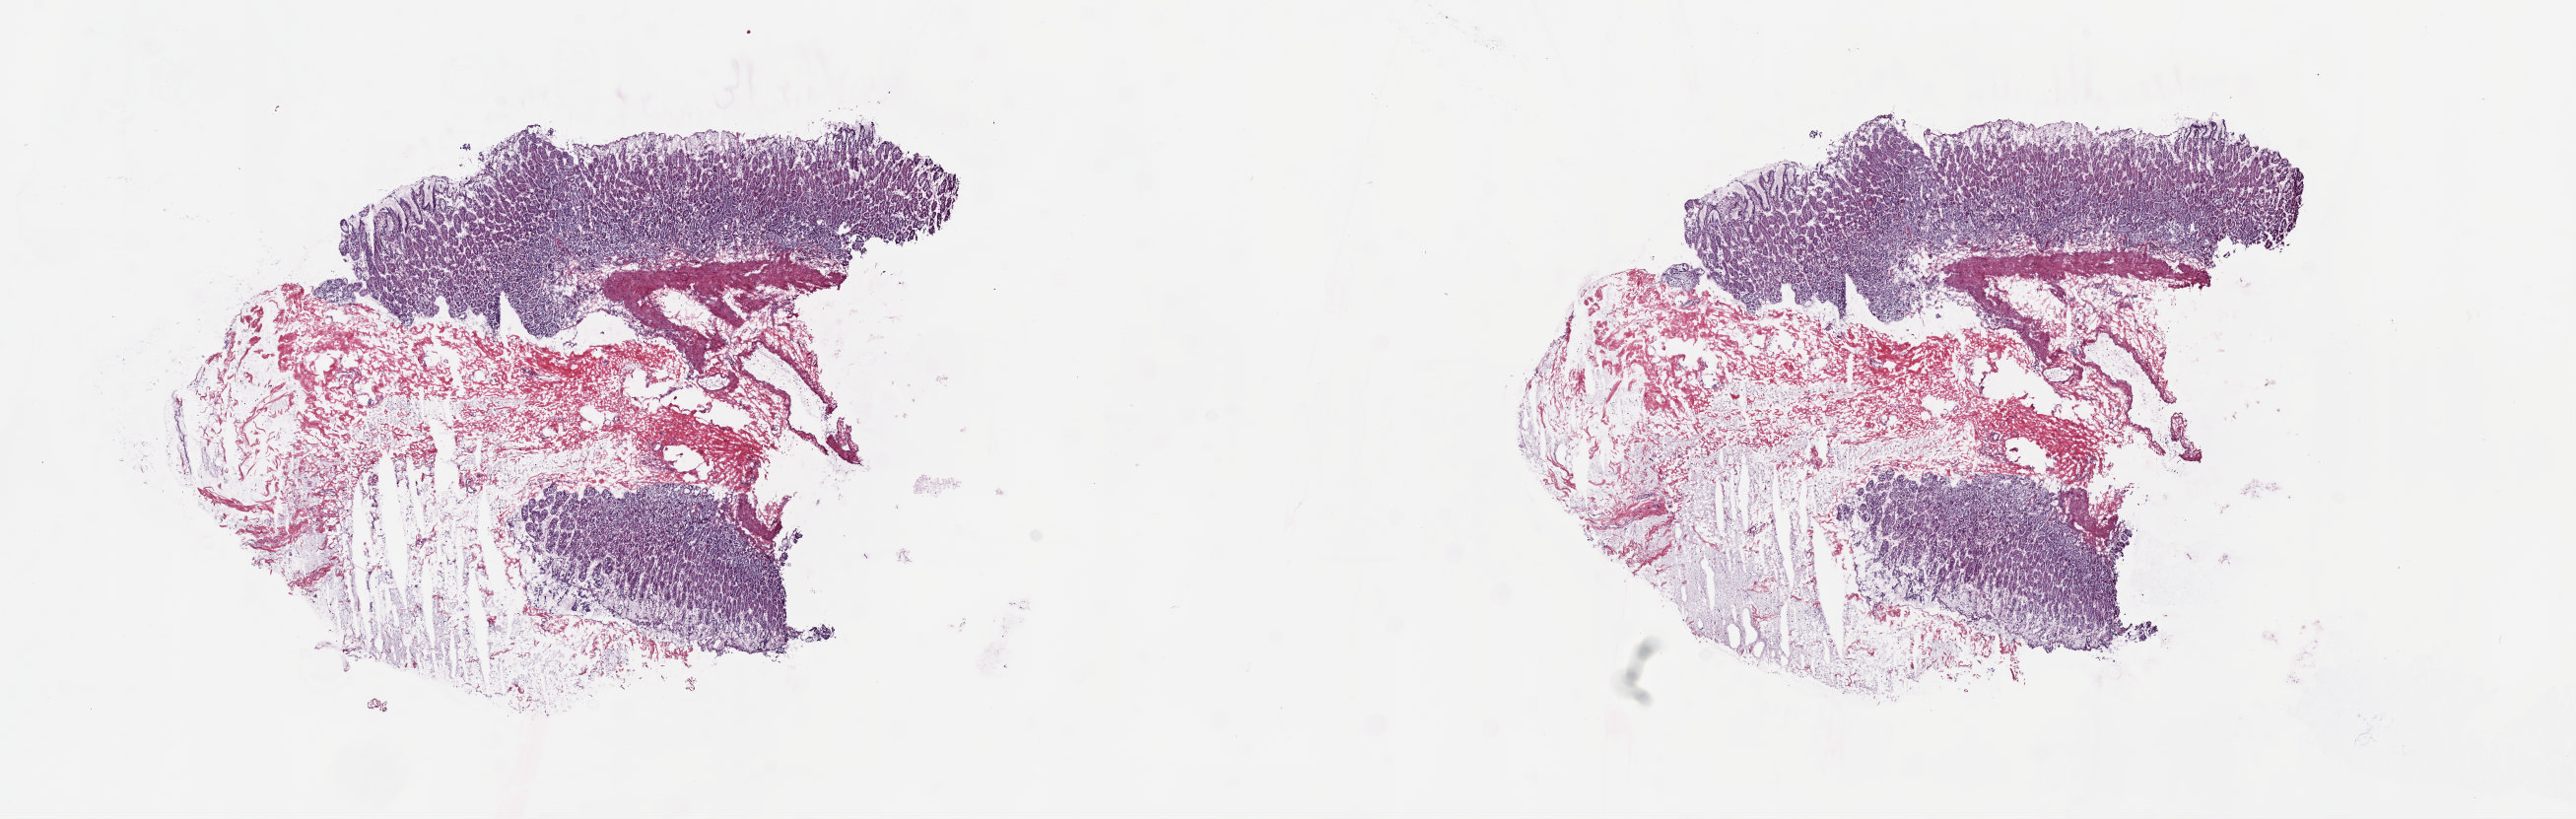
Whole-slide histology image, H&E-stained — whole scanned area (about 20.6 x 6.6 mm) shown as a low-resolution overview, frozen section, sample: solid tissue normal (non-tumour tissue), esophagus. Patient: male, age at initial diagnosis 71 years. Composition of this section per pathologist review: tumour cells 0%, tumour nuclei 0%.
This section: solid tissue normal sample (biorepository sample class). Patient diagnosis: Adenocarcinoma, NOS (lower third of esophagus).